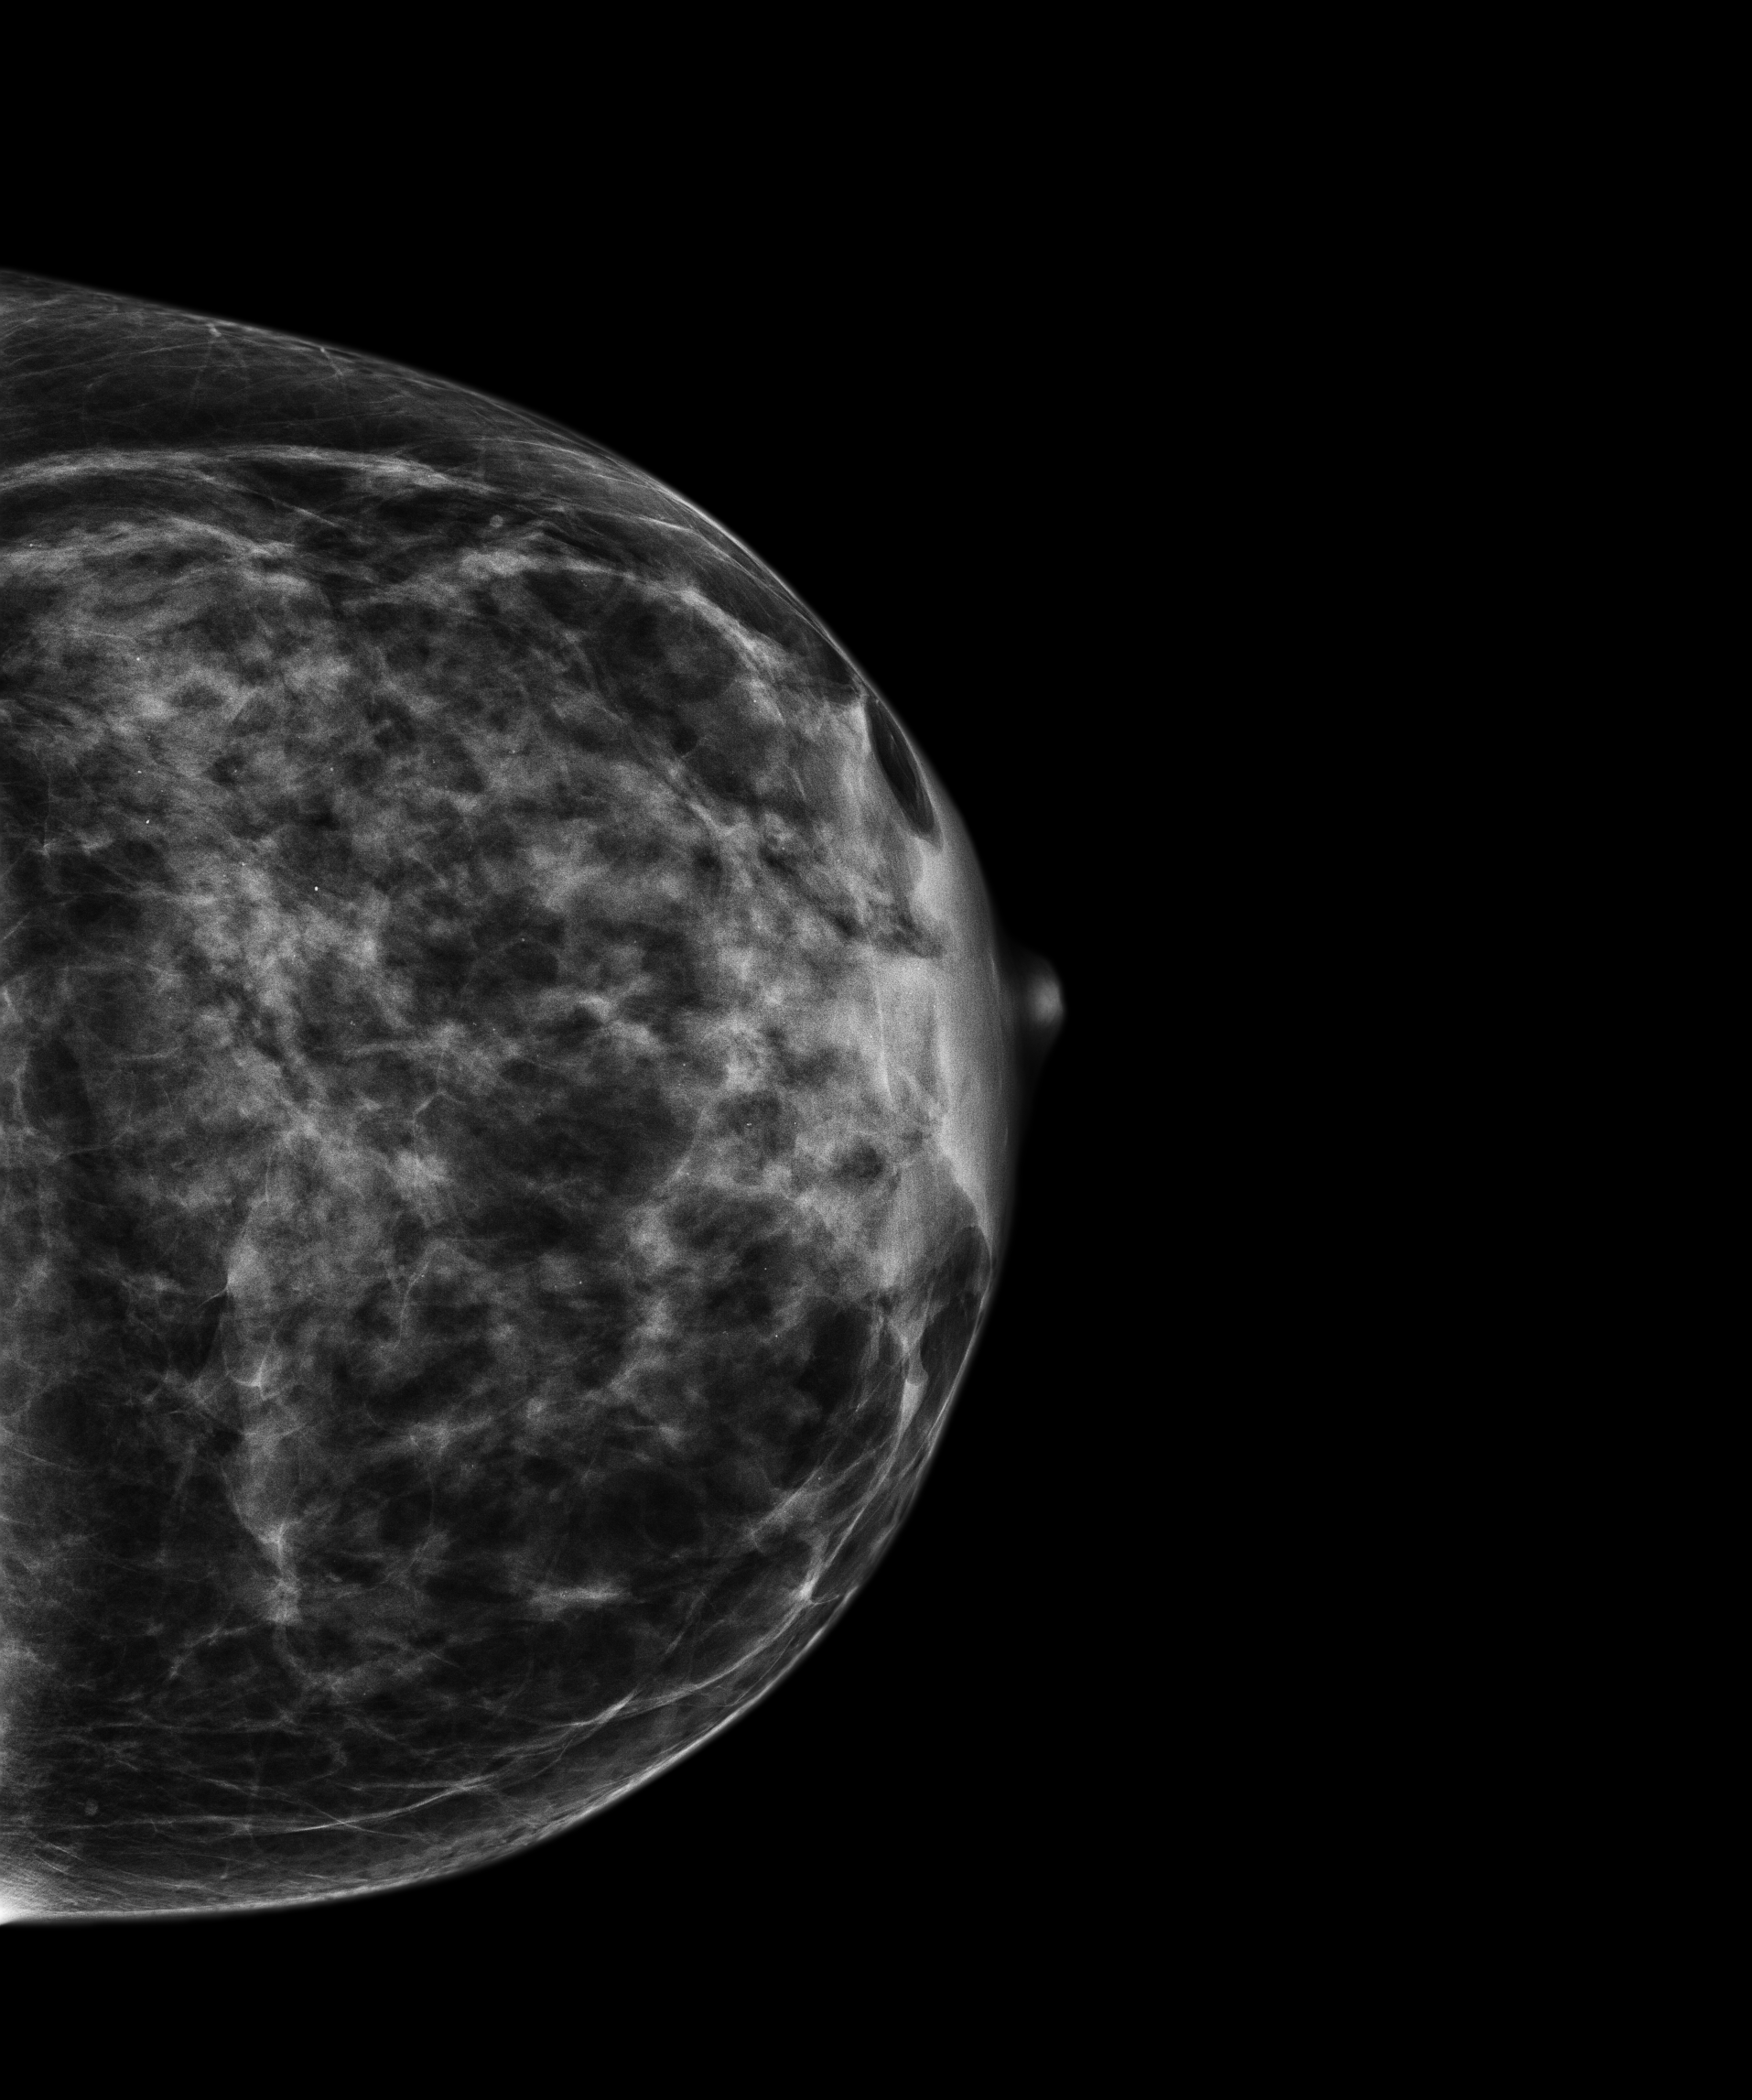
Digital mammogram (FFDM); left breast; cranio-caudal projection; screening examination; compressed breast thickness 38.3 mm. Female patient, age 47 years.
Breast density at the screening exam (both breasts): heterogeneously dense (BI-RADS density category c). Final BI-RADS category for the screening round (tomosynthesis exam, both breasts): category 3. Recall: recalled for additional imaging after this screen.